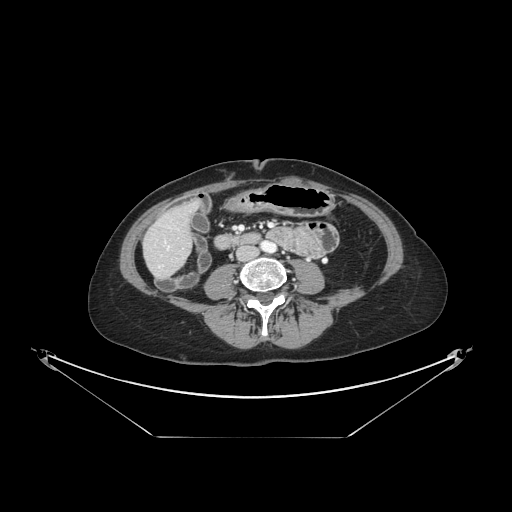
Contrast-enhanced abdominal CT, one axial slice; slice 31 of 148 in the series (ordered by position); 120 kVp; soft-tissue window (W 400 / L 40 HU); 2.5 mm slice thickness; 512 × 512 image matrix, field of view 500 × 500 mm. Female patient, age 73 years. From the clinical record (not read from this slice): diagnosis: colorectal cancer liver metastases, imaged before liver resection; multiple liver metastases: no; largest metastasis: 1 cm; chemotherapy before resection: yes.
Annotated regions visible in this slice (manually delineated by an expert):
- hepatic veins: bounding box [x1, y1, x2, y2] px = [167, 246, 169, 249]
- liver: [145, 205, 194, 277]
- planned liver remnant (the part of the liver to remain after resection): [163, 206, 193, 237]